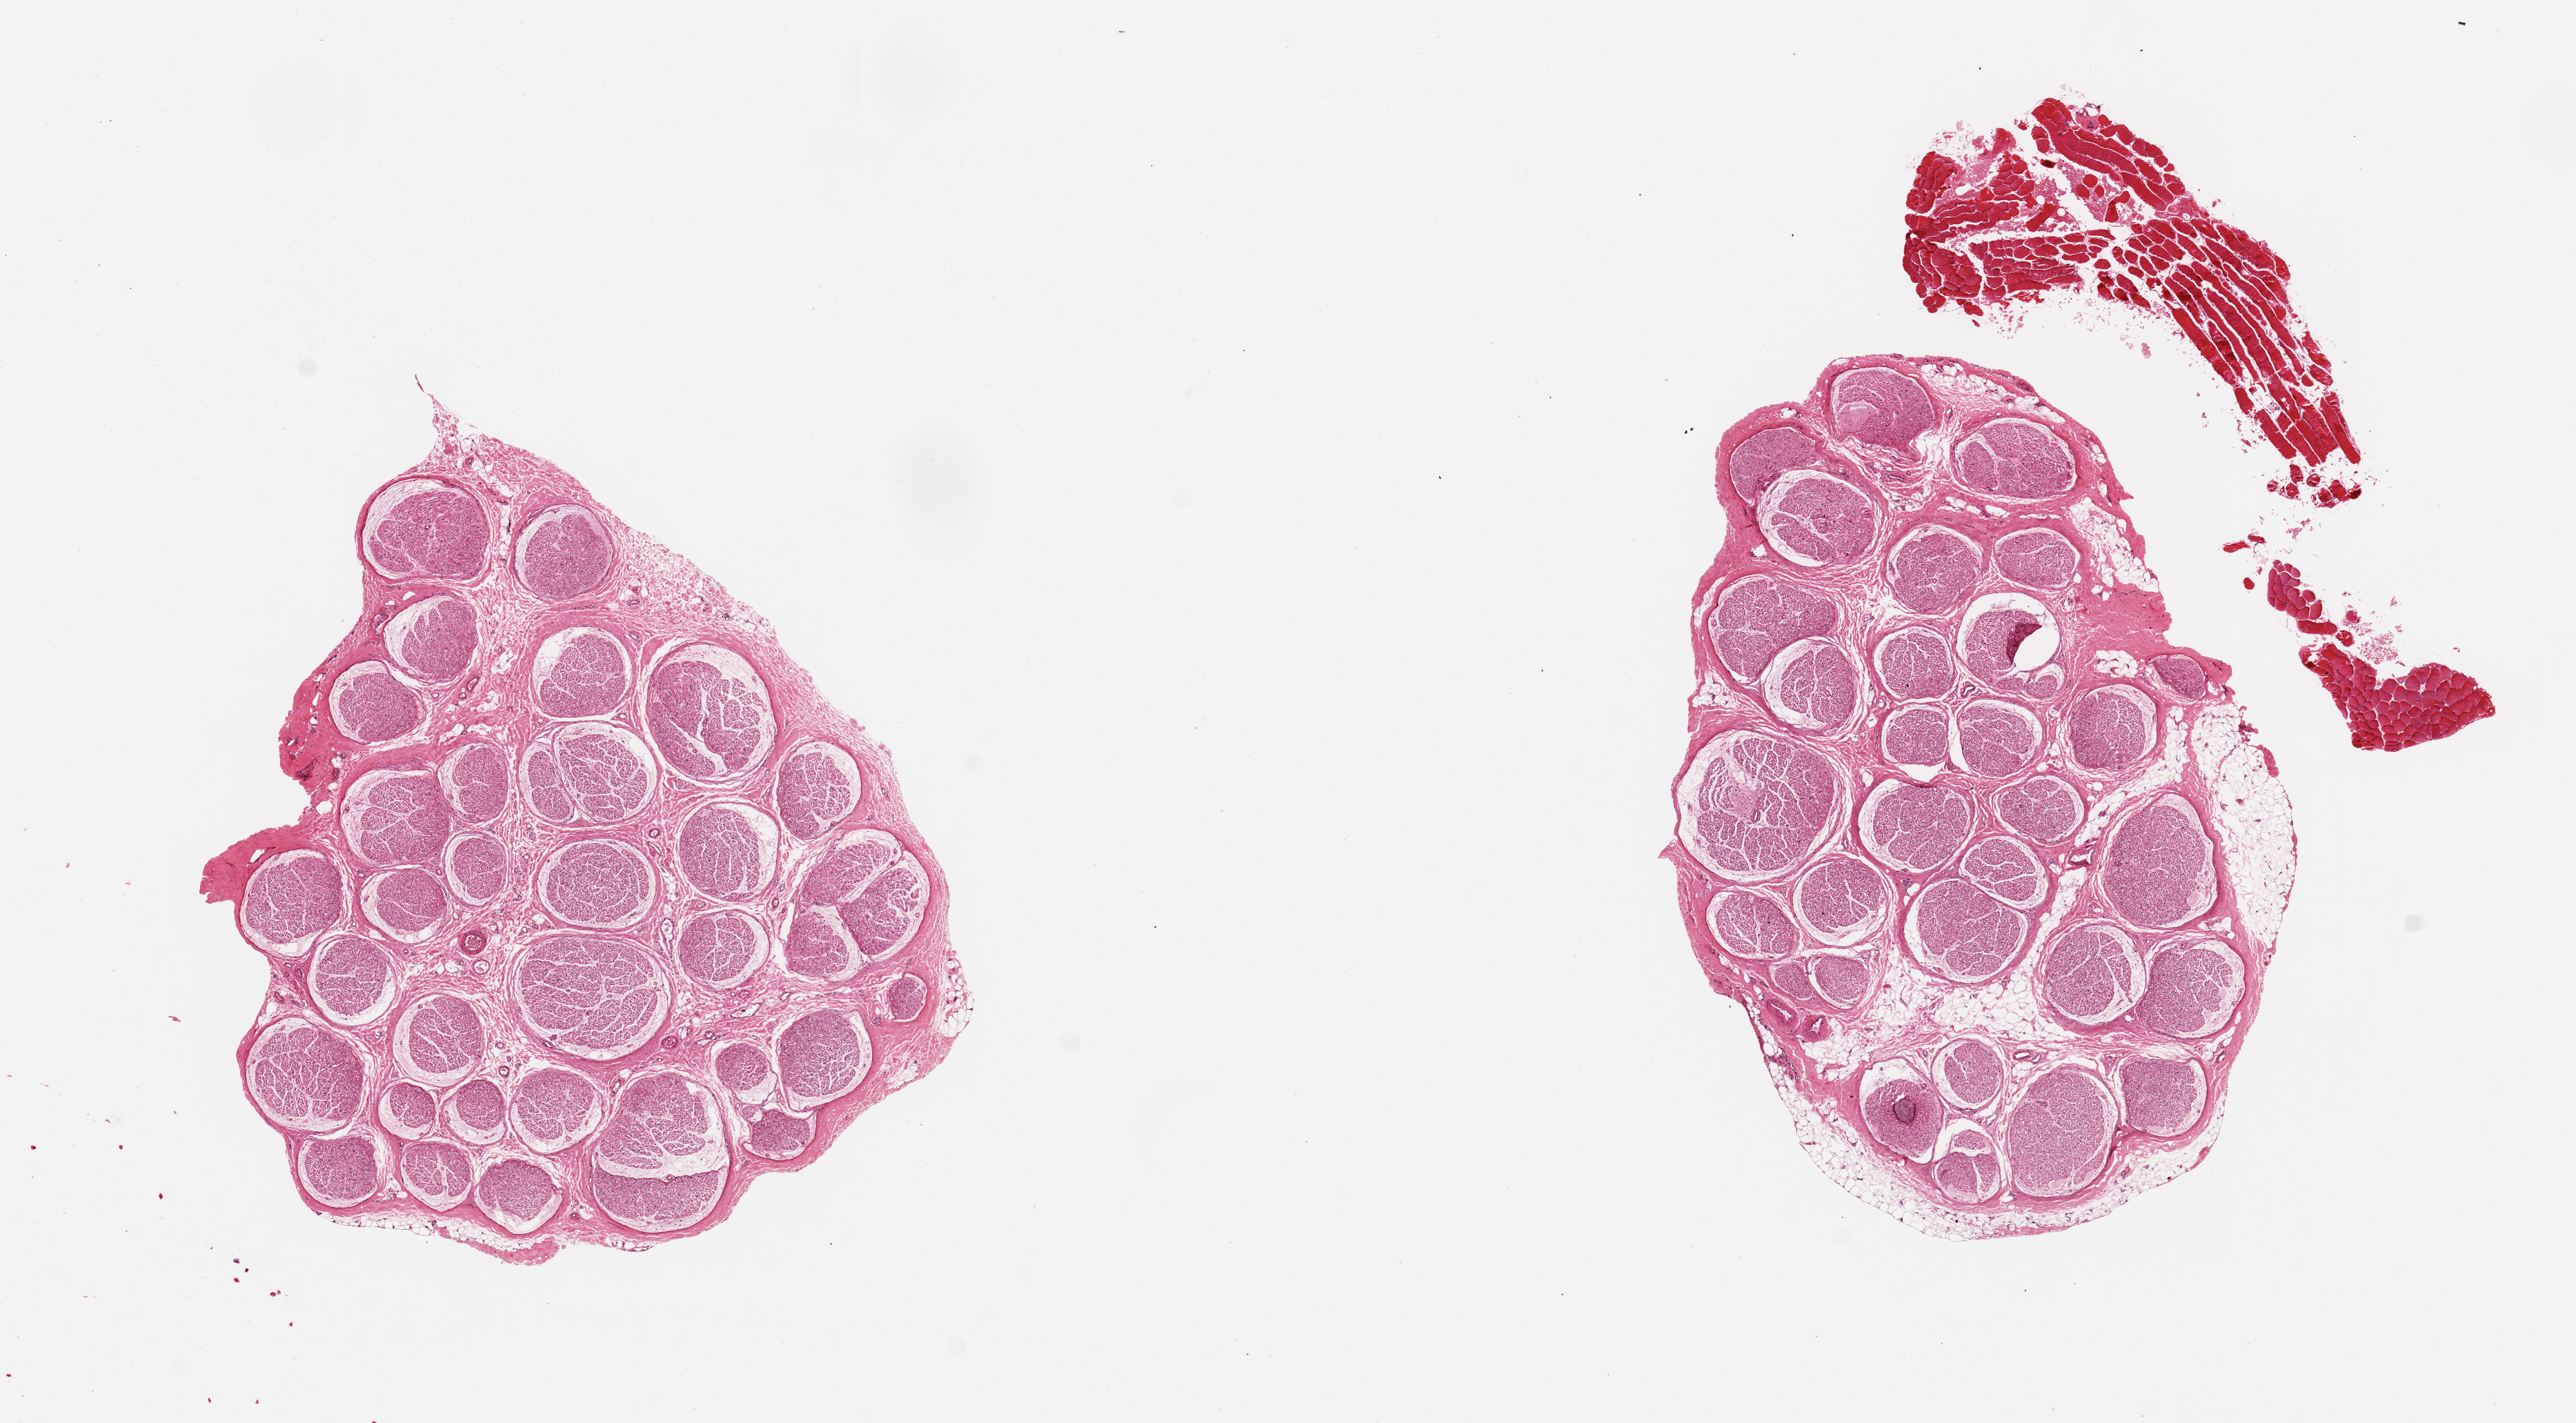
Whole-slide image, hematoxylin and eosin (H&E) stain, brightfield — low-resolution overview of the scanned area, about 14.8 x 8.2 mm. PAXgene-fixed, paraffin-embedded tissue. Target tissue: tibial nerve. Tissue donor sample.
Pathologist's review note for this sample: 2 aliquots ~5mm d. fragment of skeletal muscle near one aliquot.